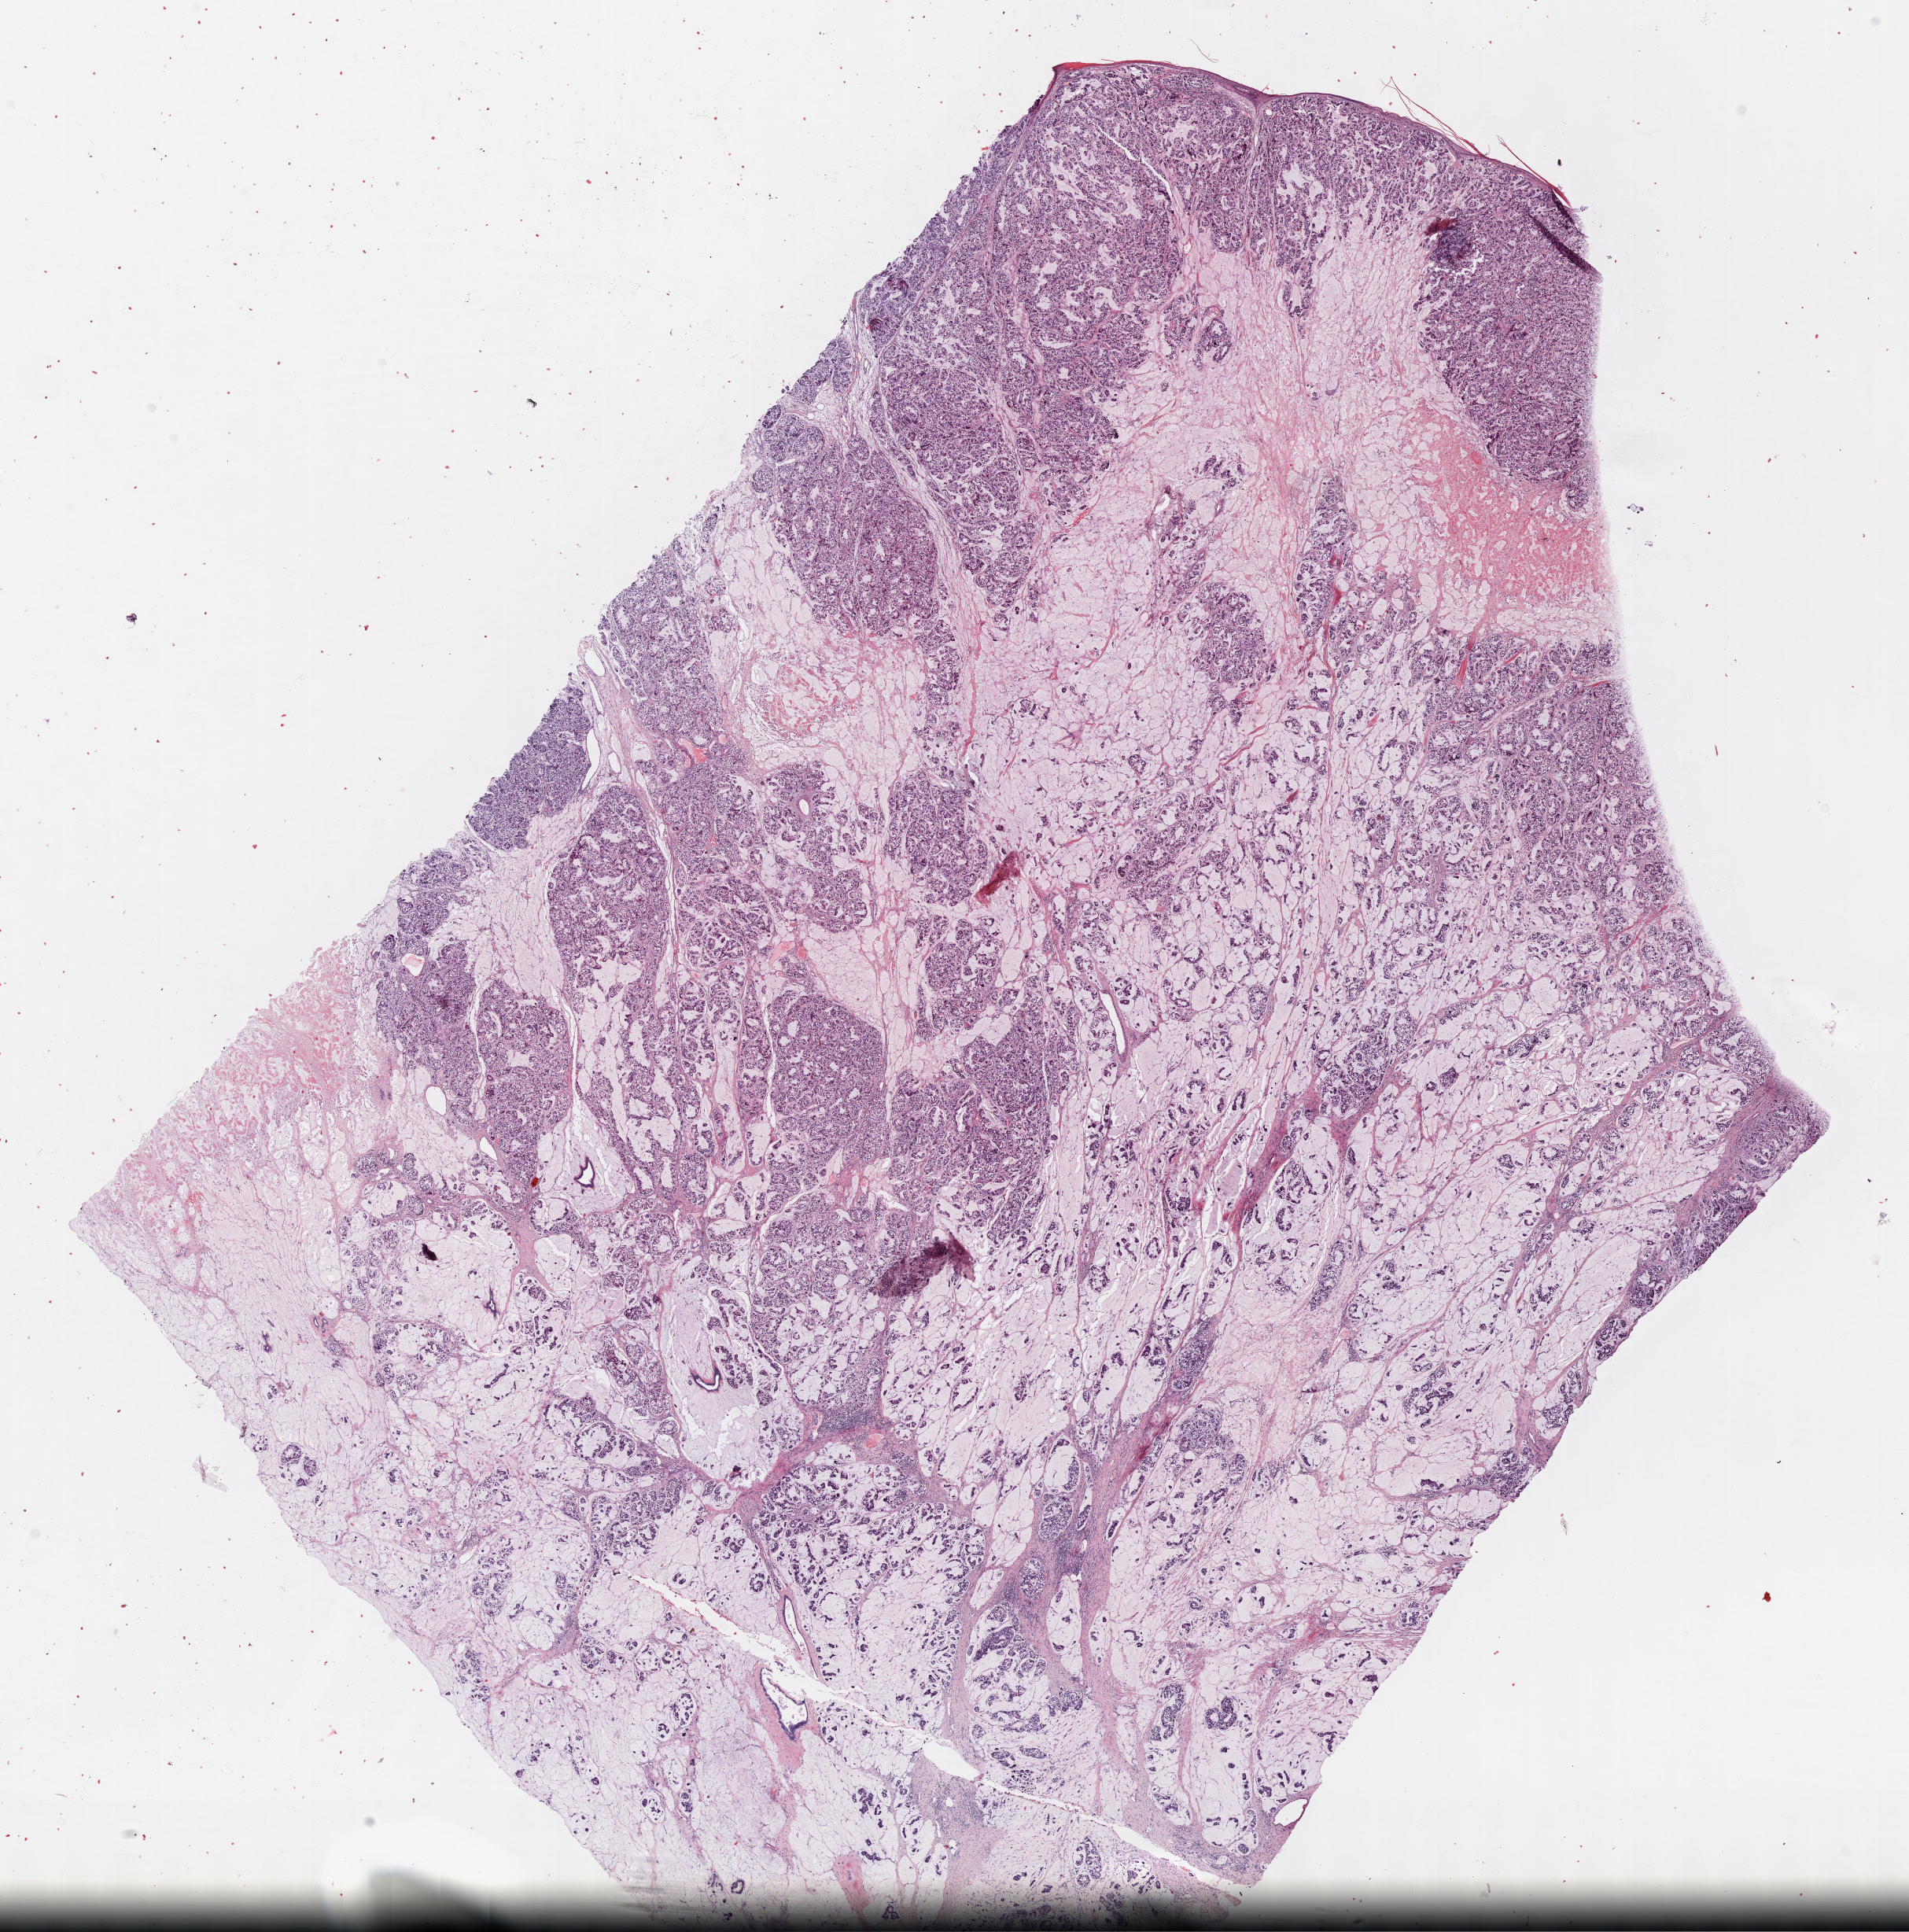
Whole-slide histology image, Hematoxylin and eosin (H&E) stained, shown as a low-resolution overview of the whole scanned area (about 19.6 x 19.9 mm, from a 40x scan), formalin-fixed paraffin-embedded (FFPE) diagnostic section, sample: primary tumour, breast. Female, age 55 years at initial diagnosis.
AJCC pathologic stage: IIIB (7th edition). Histologic diagnosis: Mucinous adenocarcinoma.